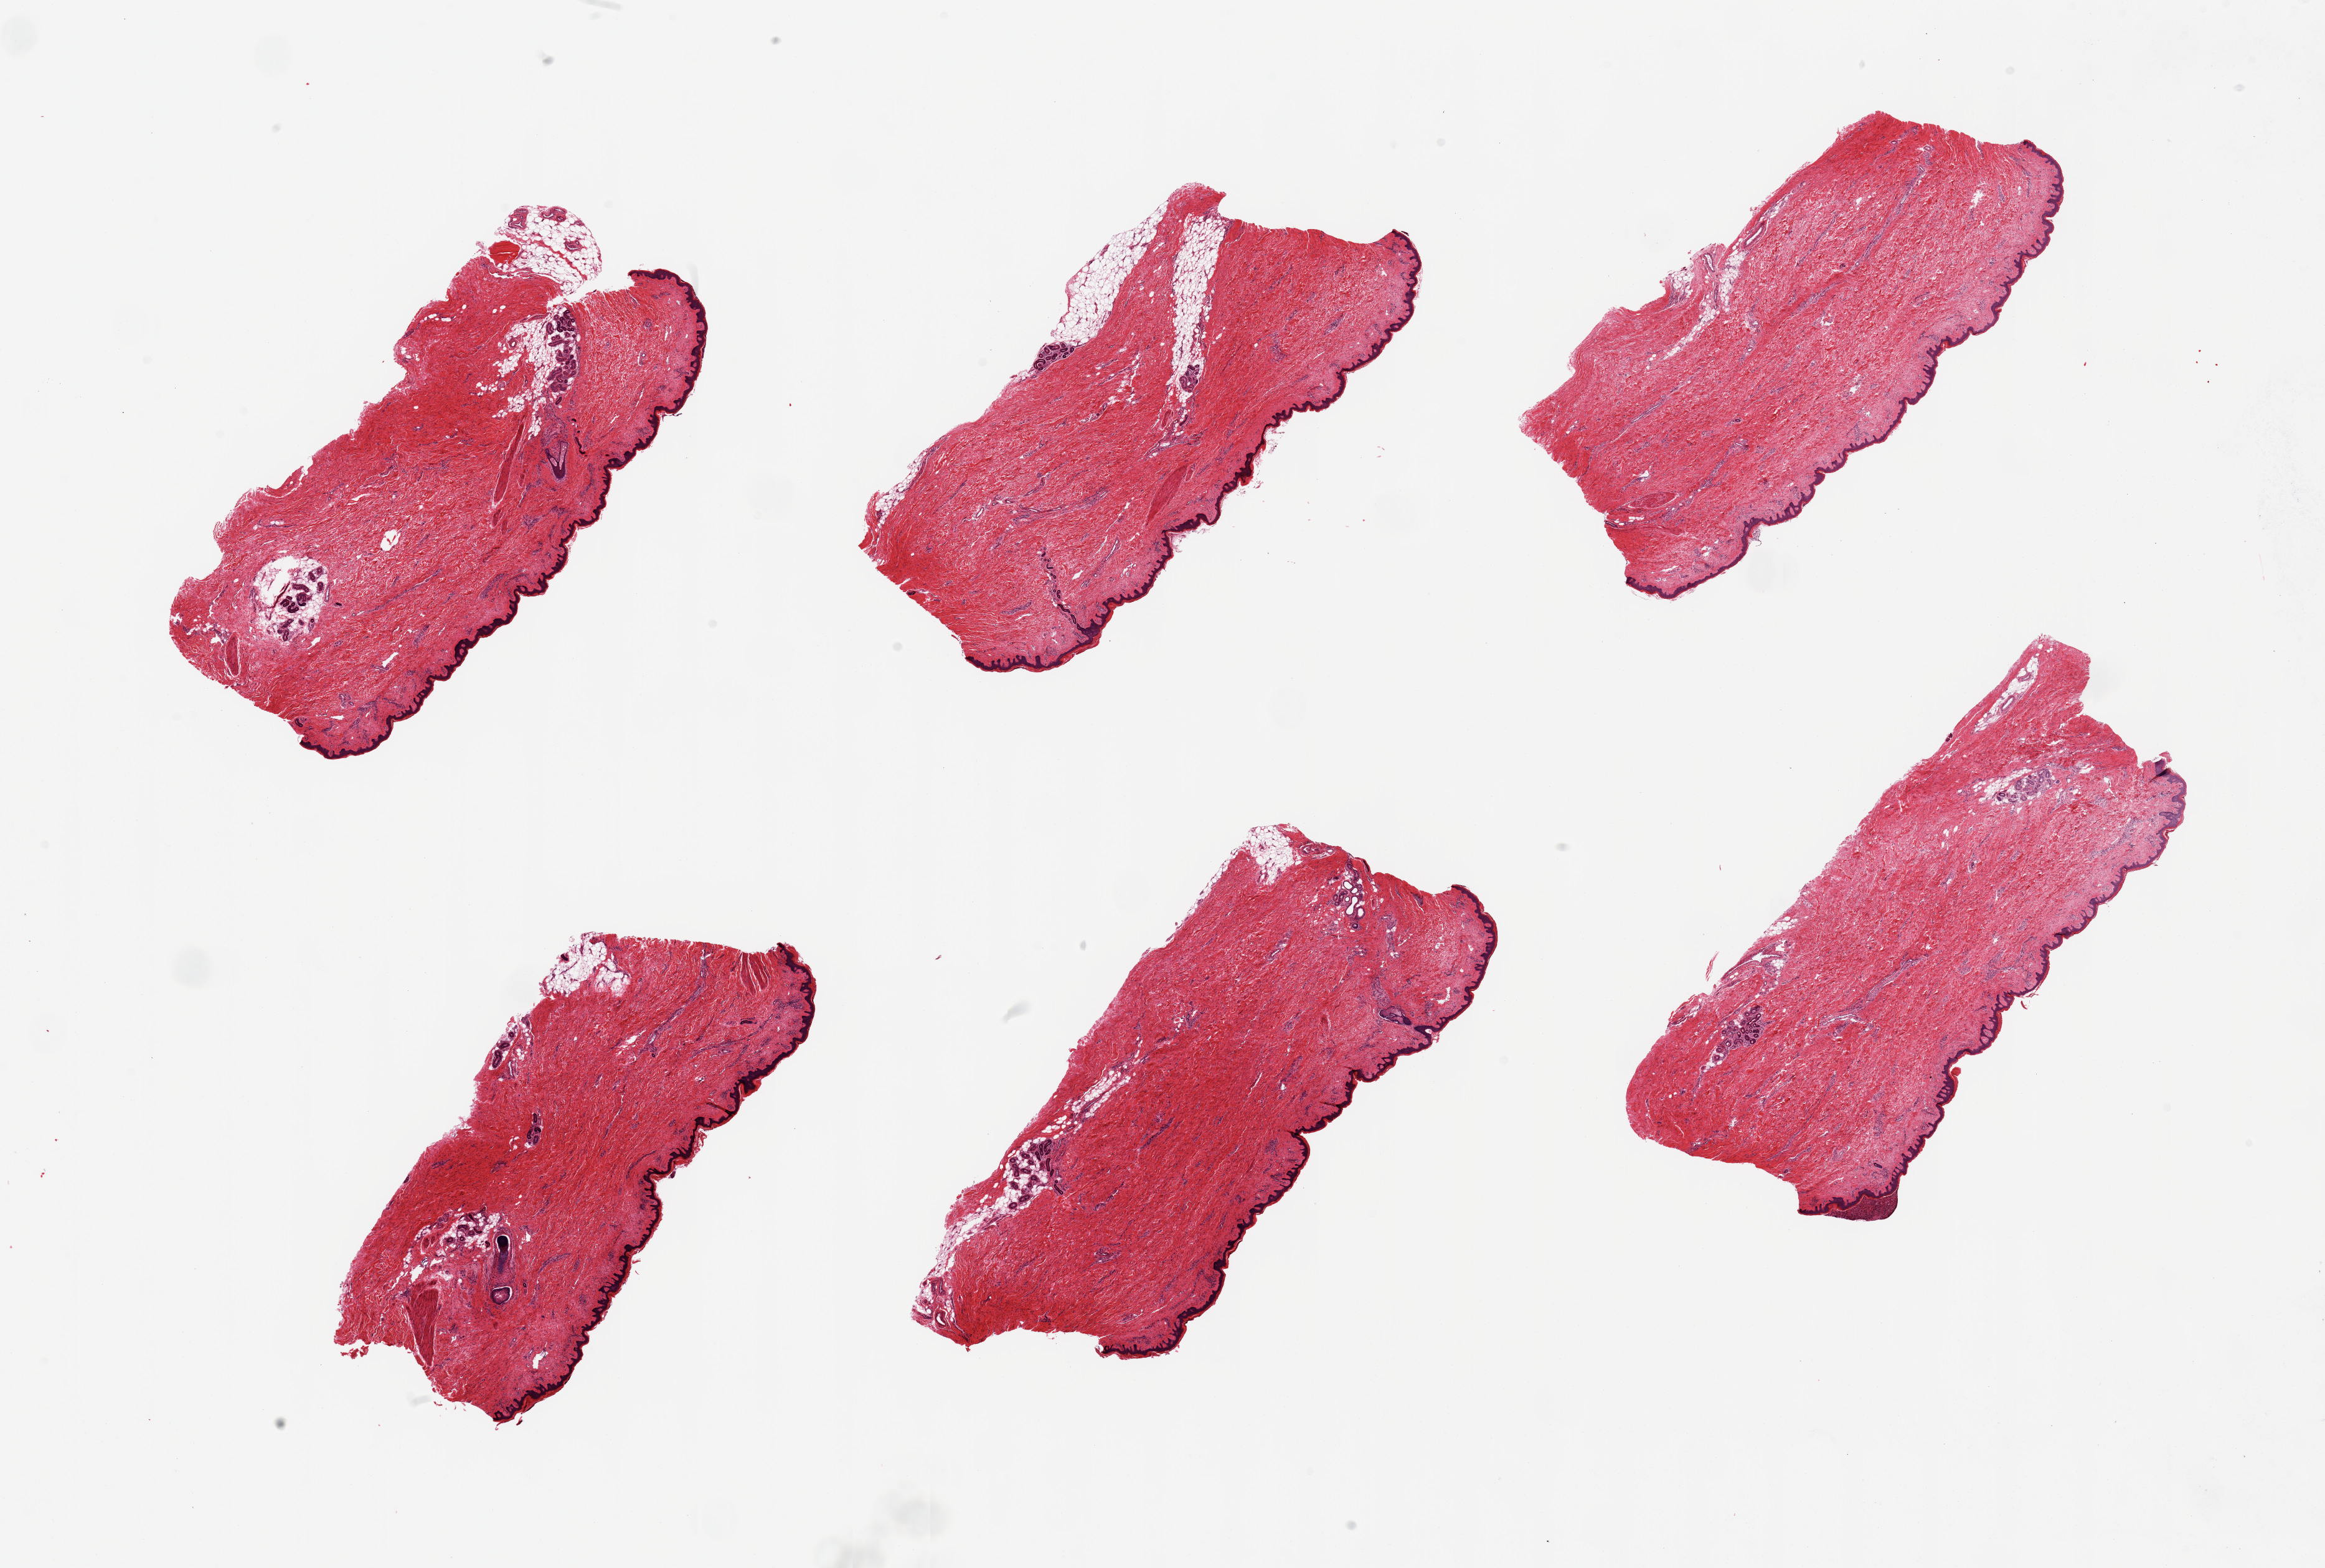
Whole-slide image, H&E stain, whole scanned area (about 29.5 x 19.9 mm) shown as a low-resolution overview, PAXgene-fixed paraffin-embedded (PFPE) section, sampled site (target tissue): skin of suprapubic region, donor tissue sample. Donor: female.
Review note (as recorded): 6 pieces; well trimmed; 5-10% intradermal fat.